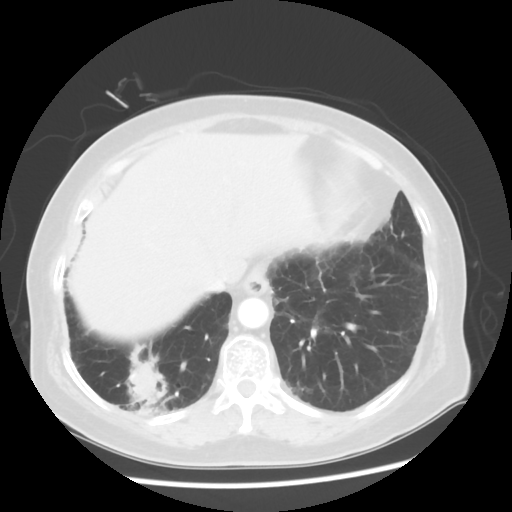
Chest CT, one axial slice; position 14 of 56 along the scan axis; reconstruction kernel STANDARD; lung window (W 1500 / L -600 HU); 5 mm slice thickness; 512 × 512 image matrix, field of view 360 × 360 mm. Female patient, age 64 years. Case-level facts recorded for this patient, not image findings: clinical TNM (as recorded): Tis N0 M0.
Structures marked on this image (rectangle marked by the reading radiologist):
- lung tumour (recorded histology: adenocarcinoma): bounding box (x1, y1, x2, y2) in pixels: (107, 340, 176, 424)